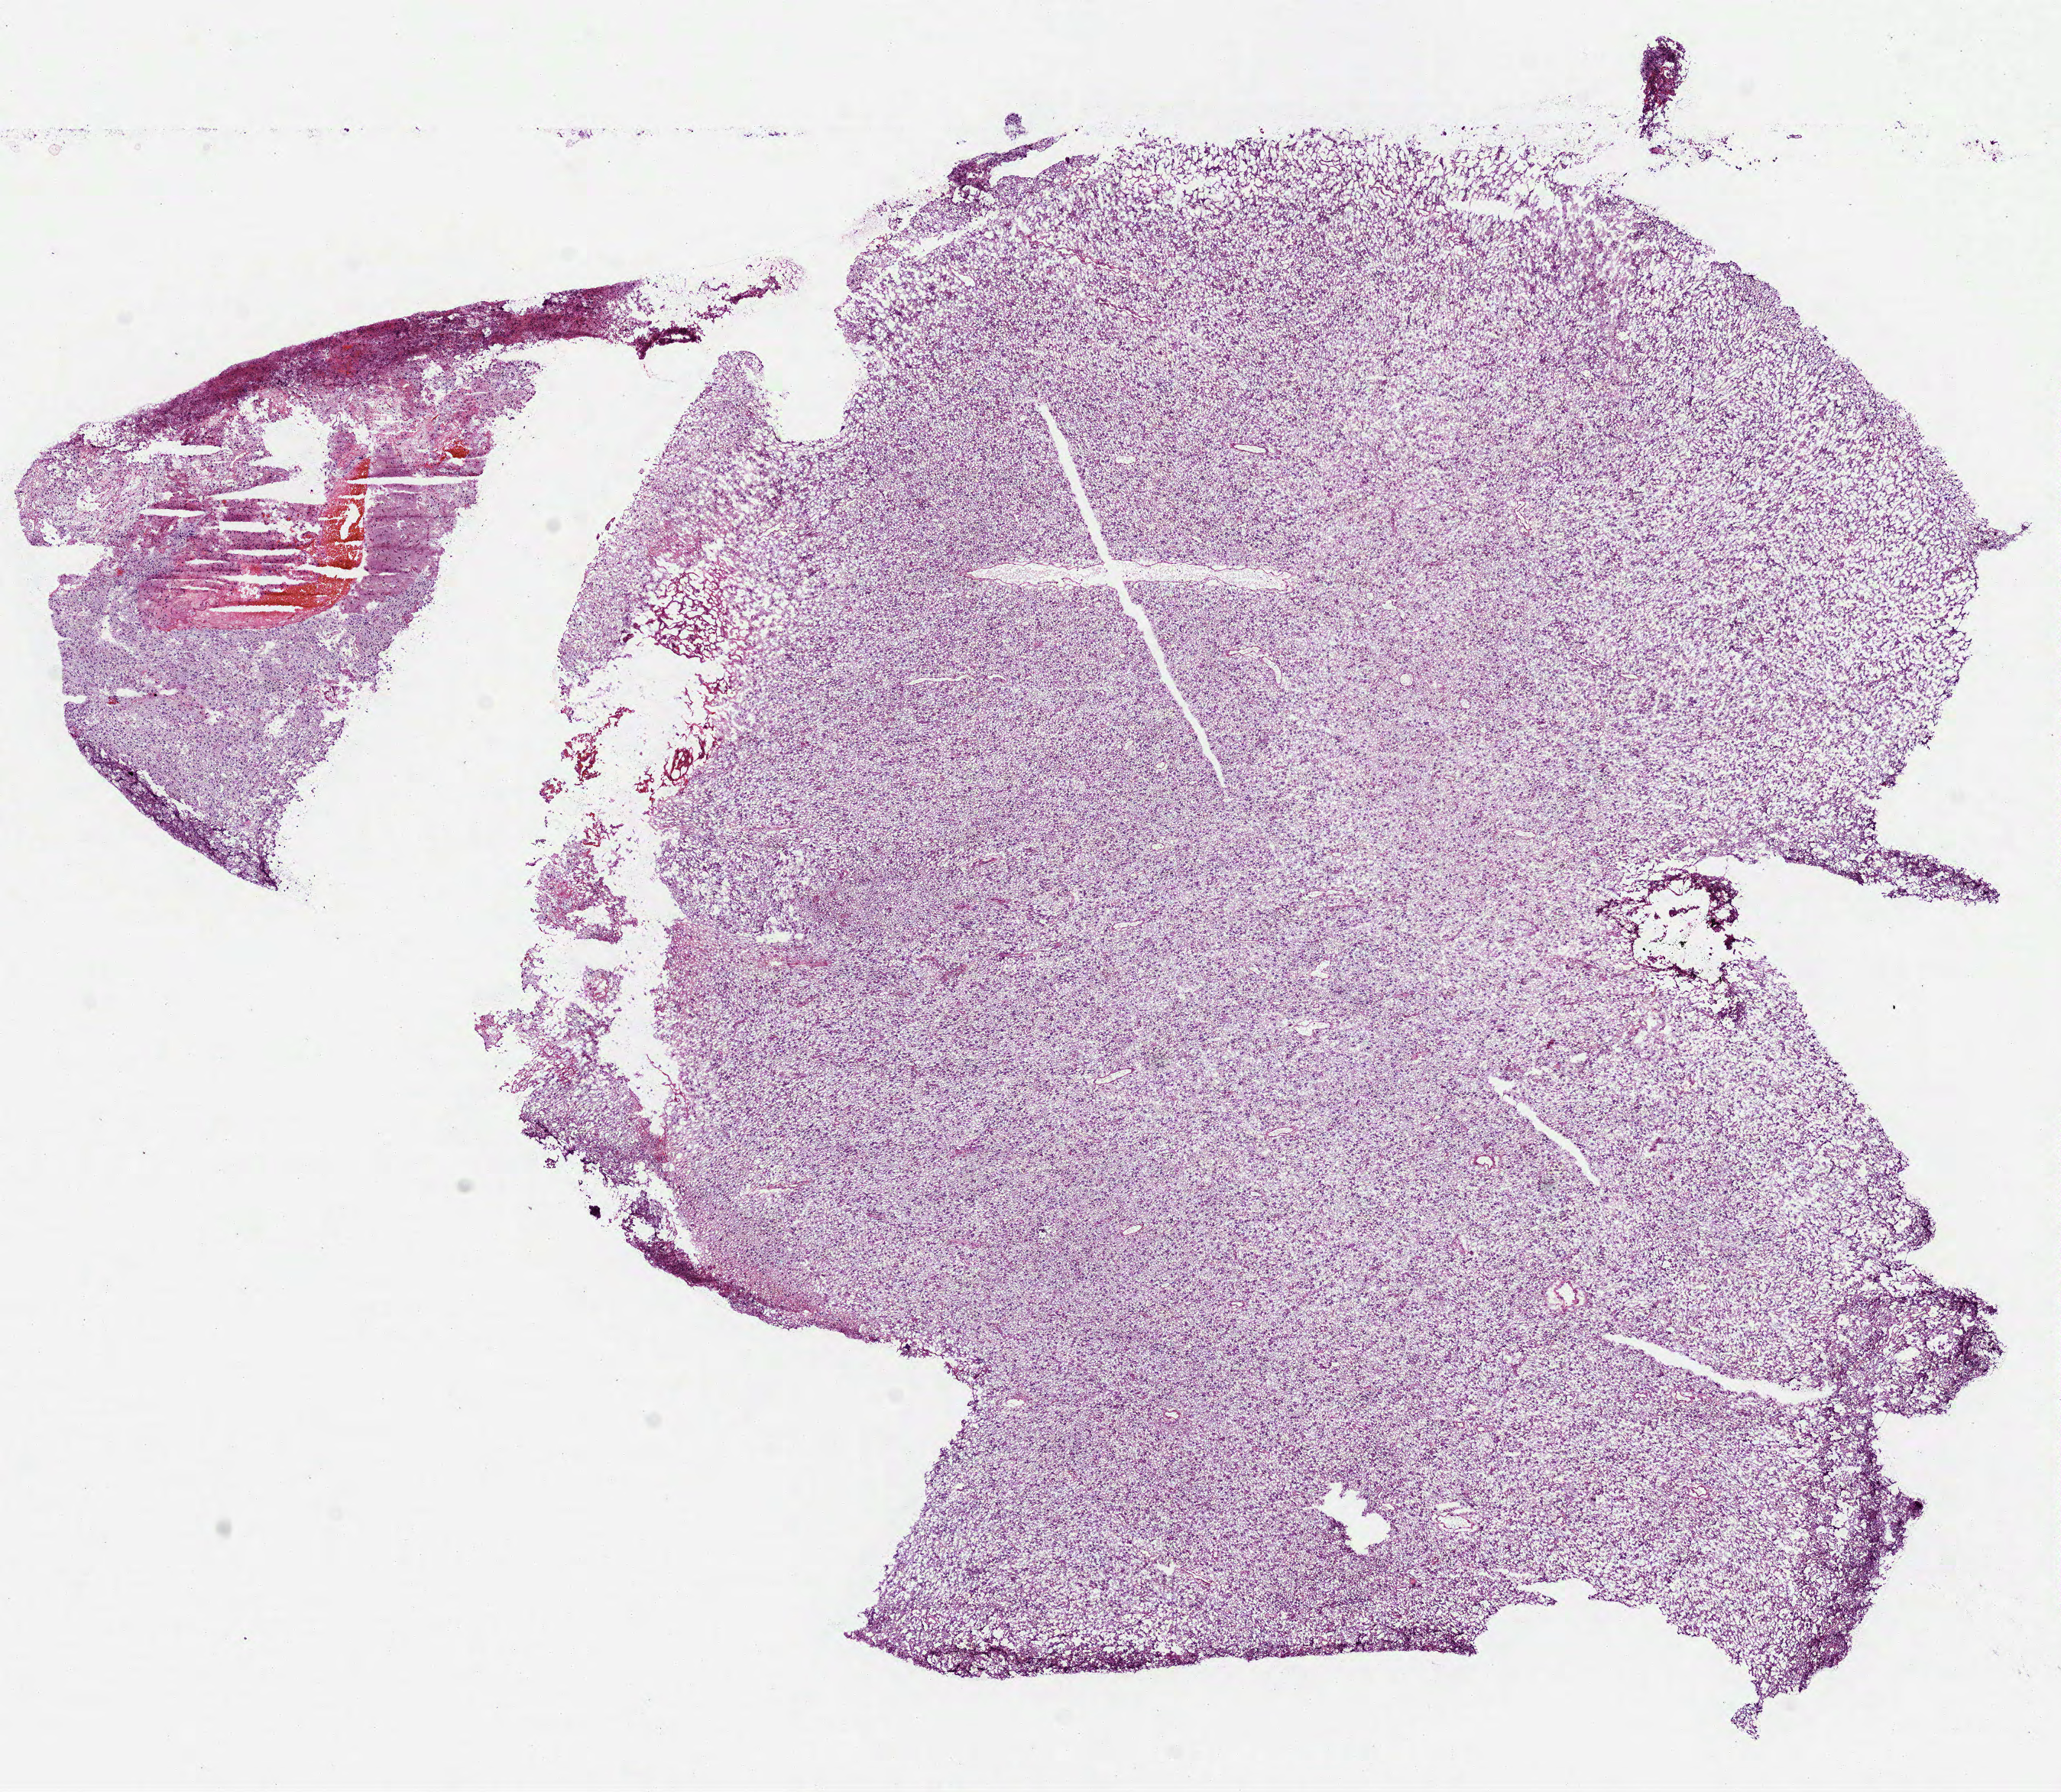
Whole-slide histology image, Hematoxylin and eosin (H&E) stained, whole scanned area (about 10.9 x 9.5 mm) shown as a low-resolution overview. Frozen section. Sample: primary tumour, brain. Male patient; age at initial diagnosis 14 years.
Histologic diagnosis: Mixed glioma (cerebrum).